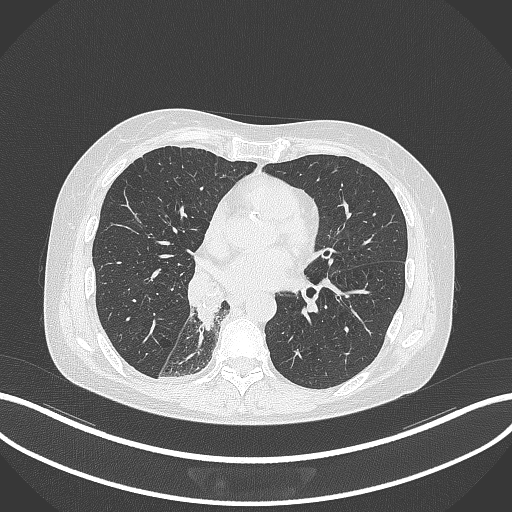
Chest CT, one axial slice; slice 141 of 329 in the series (ordered by position); 120 kVp; lung window (W 1500 / L -600 HU); 1 mm slice thickness; 512 × 512 image matrix, field of view 400 × 400 mm. Female patient, age 63 years. Case-level facts recorded for this patient, not image findings: clinical TNM (as recorded): T1c N0 M0.
Outlined on this slice (bounding box drawn by a radiologist):
- lung tumour (recorded histology: adenocarcinoma): bounding box <194,279,221,334> (left, top, right, bottom; pixels)